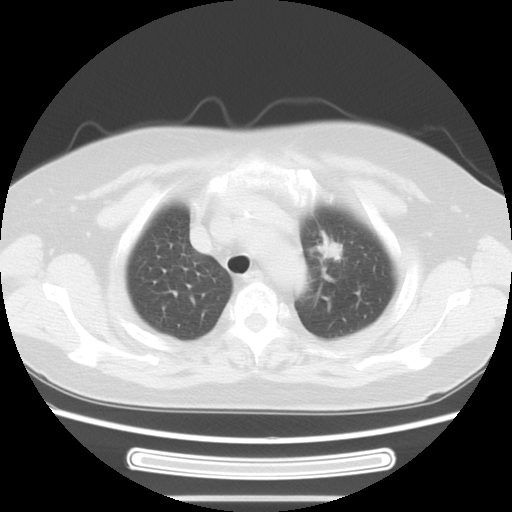
Chest CT, one axial slice; slice 47 of 58 in the series (ordered by position); reconstruction kernel STANDARD; lung window (W 1500 / L -600 HU); 5 mm slice thickness; 512 × 512 image matrix, field of view 350 × 350 mm. Female patient, age 70 years. From the clinical record (not read from this slice): clinical TNM (as recorded): T1c N0 M0; histopathological grade: G2-3.
Structures marked on this image (bounding box drawn by a radiologist):
- lung tumour (recorded histology: adenocarcinoma): bounding box <313,223,342,270> (left, top, right, bottom; pixels)